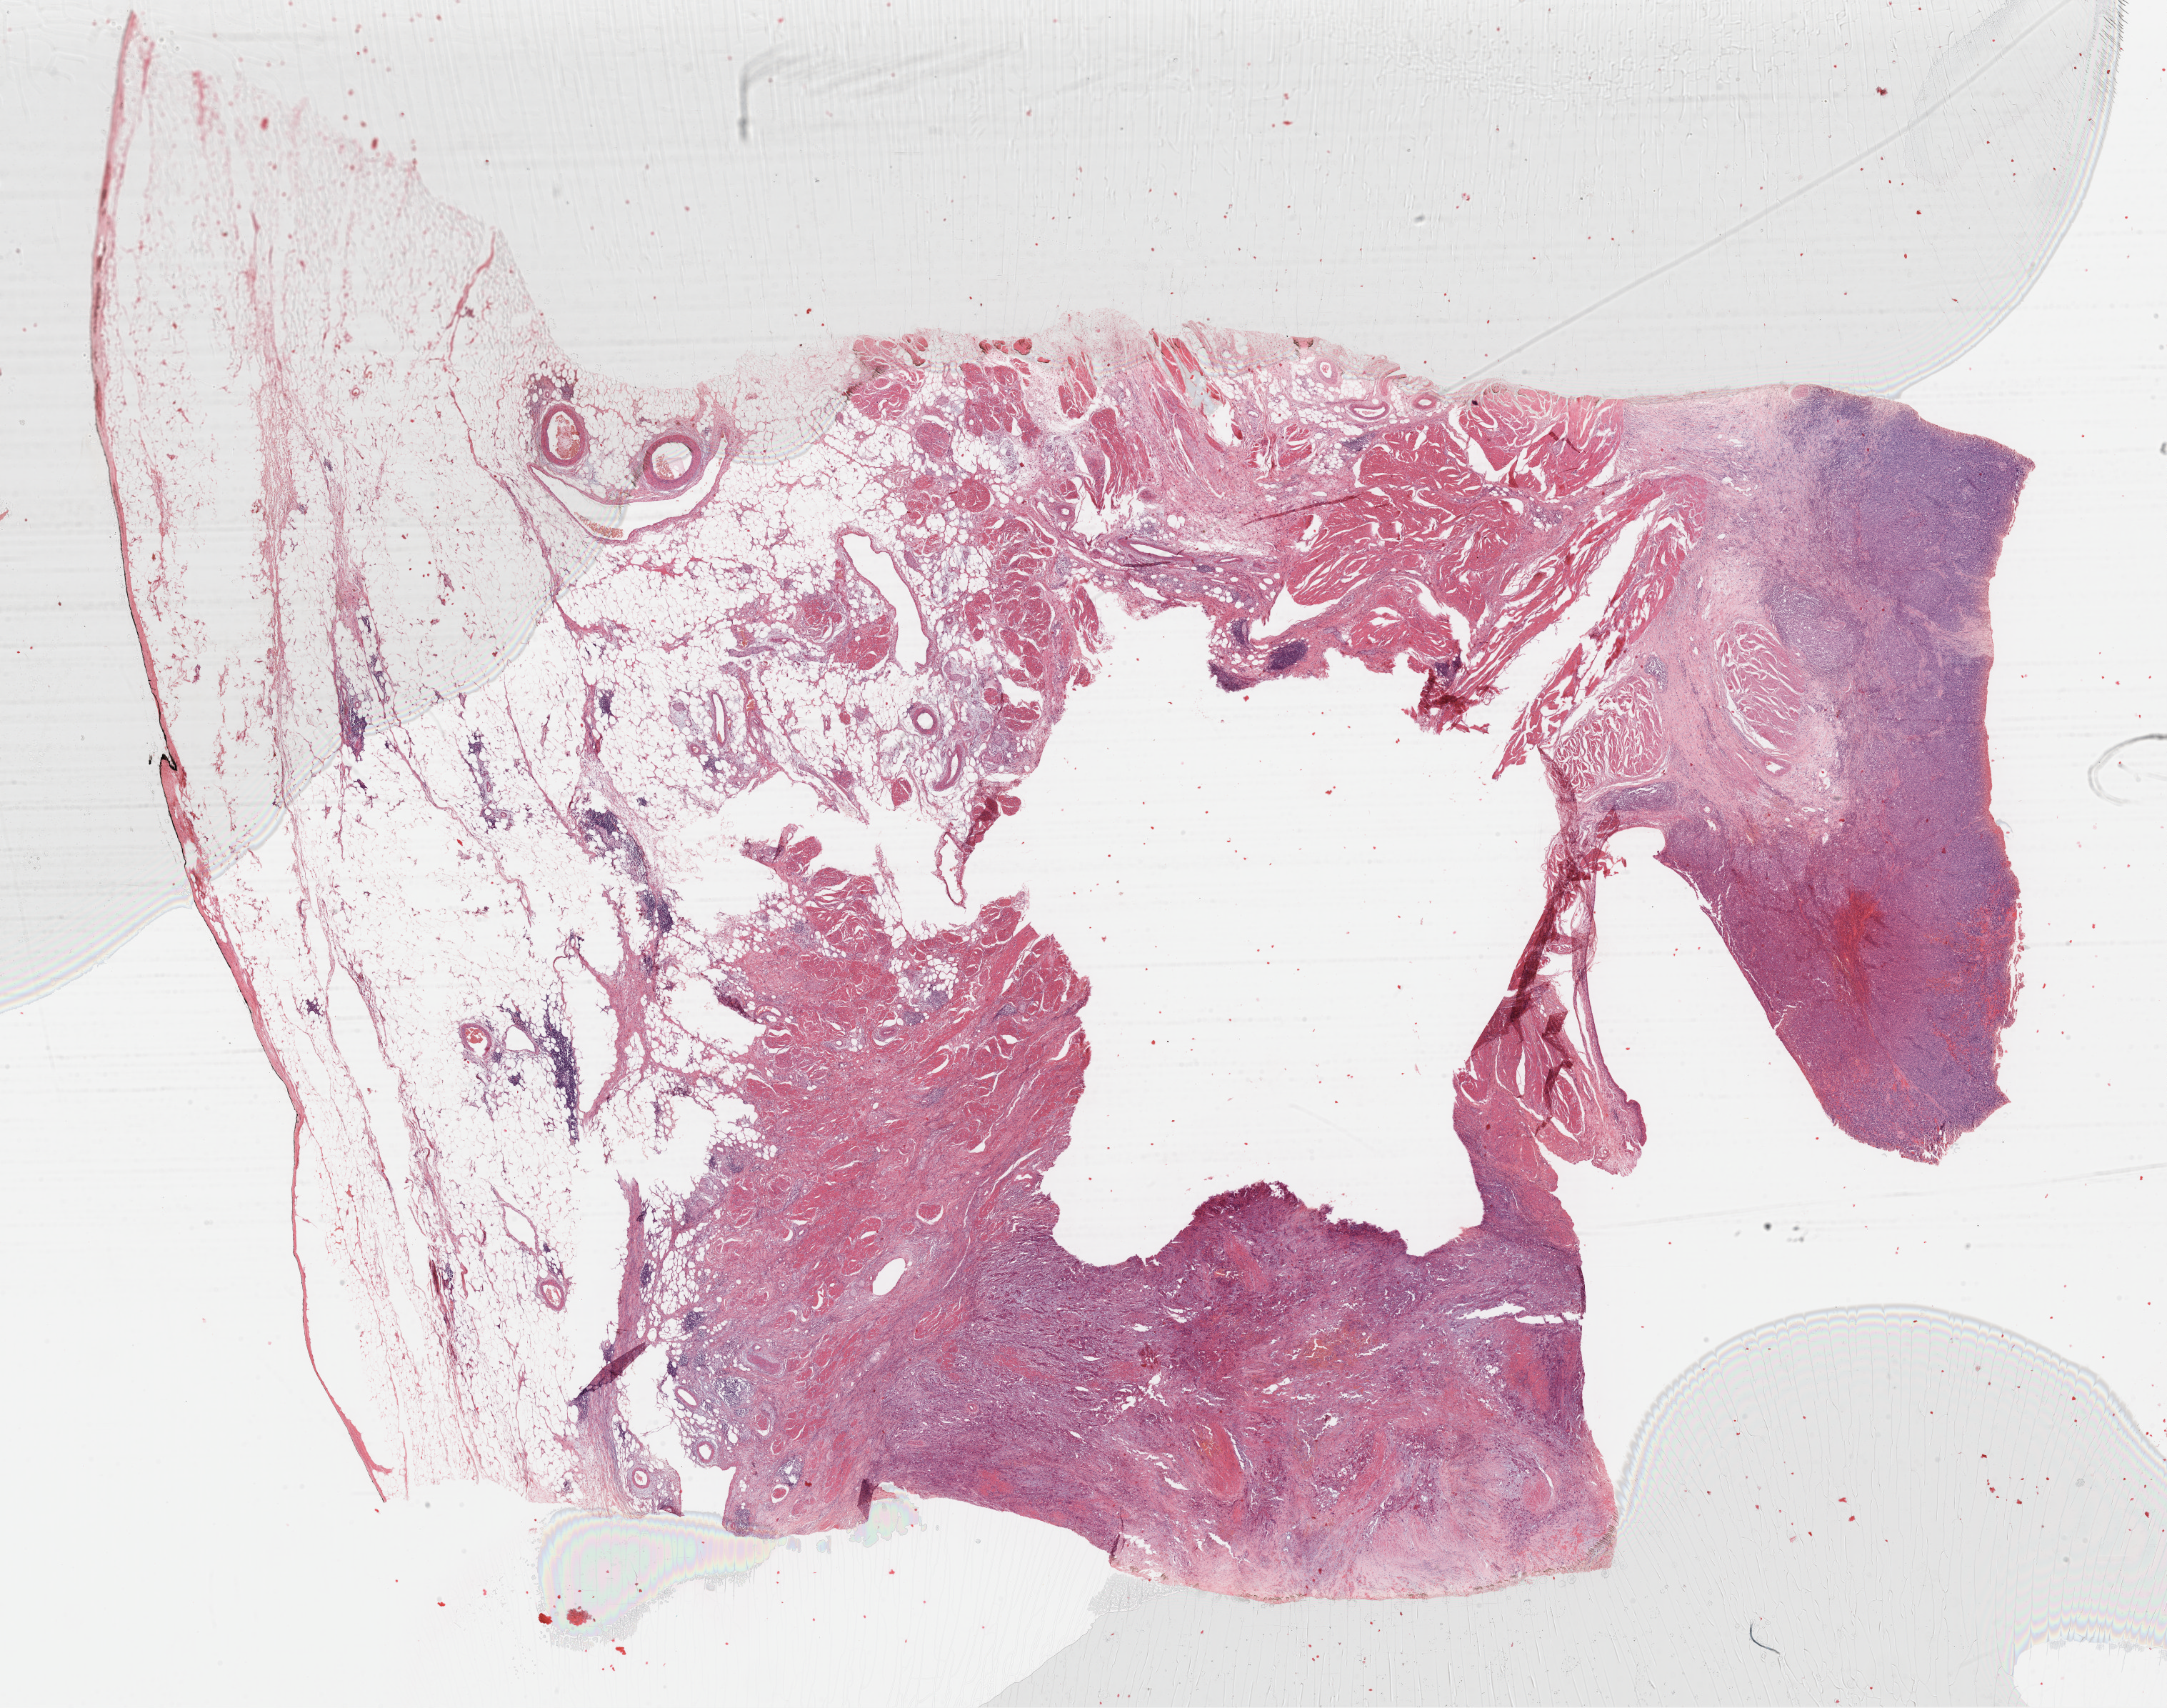
H&E-stained whole-slide image, shown as a low-resolution overview of the whole scanned area (about 24.0 x 18.9 mm), FFPE section, bladder, primary tumour sample. Male patient; age at initial diagnosis 75 years. Histologic grade: high grade.
Histologic diagnosis: Transitional cell carcinoma (posterior wall of bladder). AJCC pathologic stage: II (5th edition). Lymph nodes positive (case pathology): 0 of 17 examined.